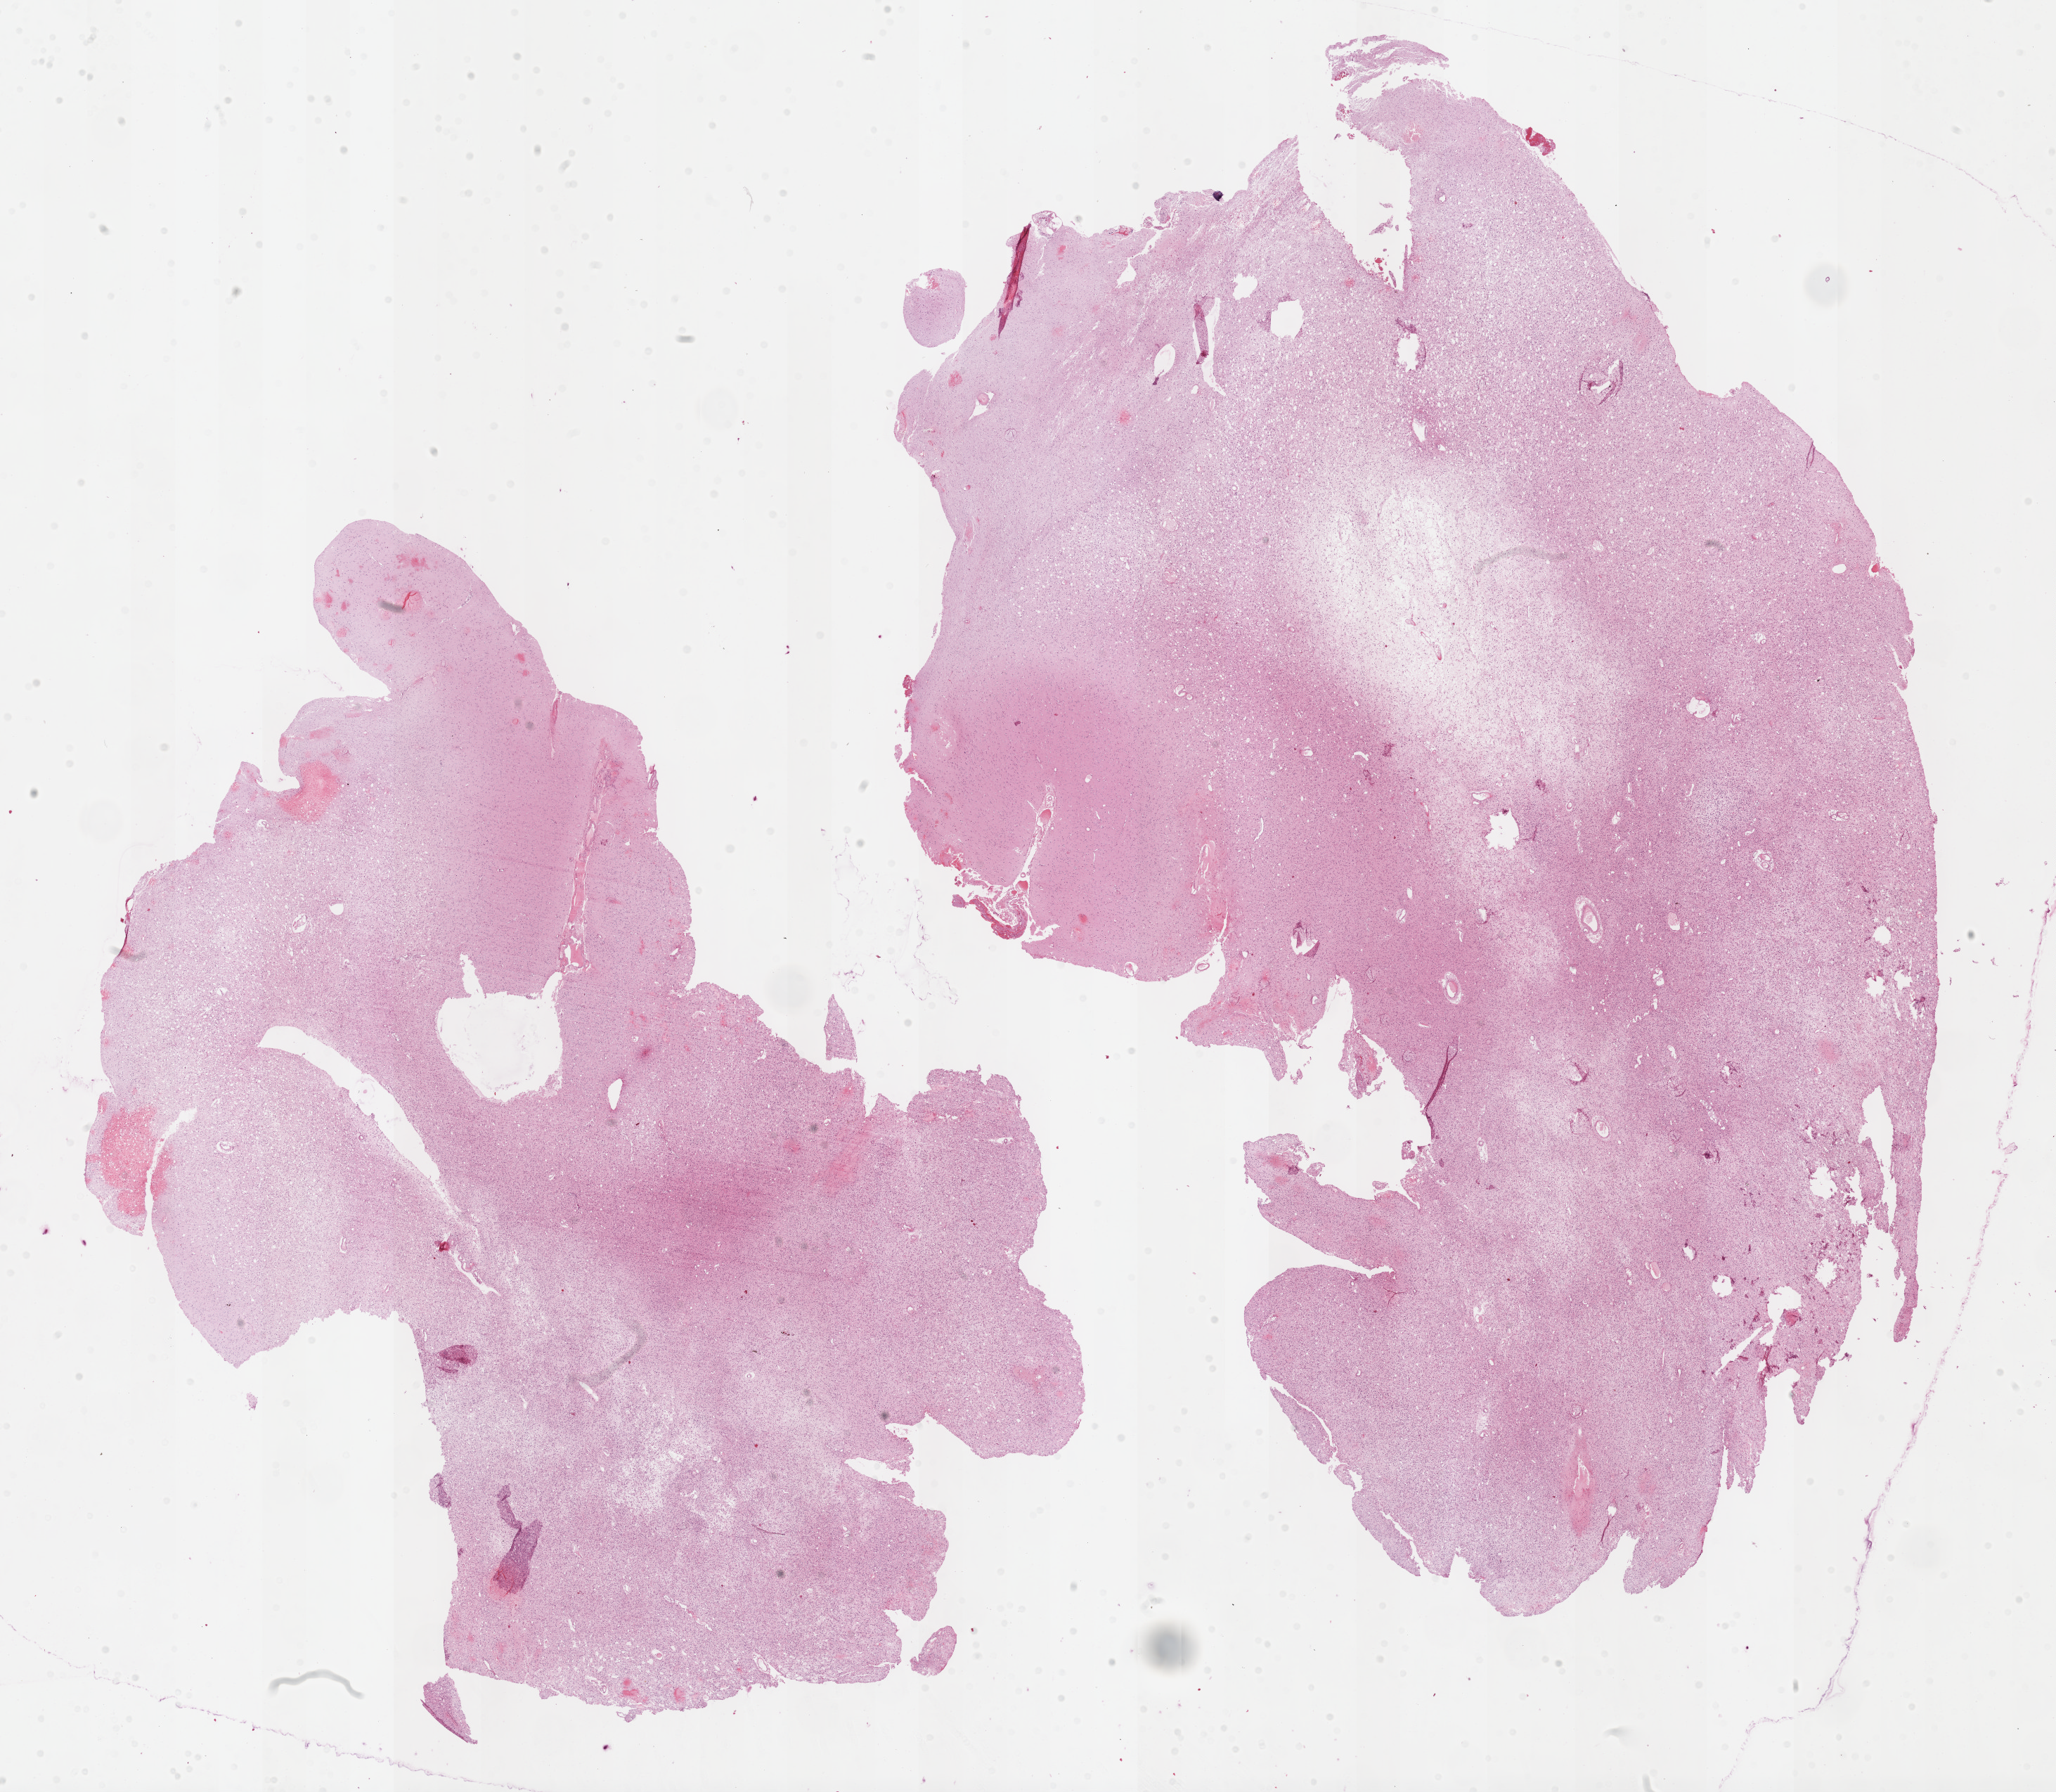
Whole-slide histology image, H&E — shown as a low-resolution overview of the whole scanned area (about 23.7 x 20.6 mm, slide scanned at 40x). FFPE section. Brain, primary tumour sample. Male, age 27 years at initial diagnosis. Histologic grade: G2 (moderately differentiated).
* histologic diagnosis: Mixed glioma (cerebrum)
* laterality: right